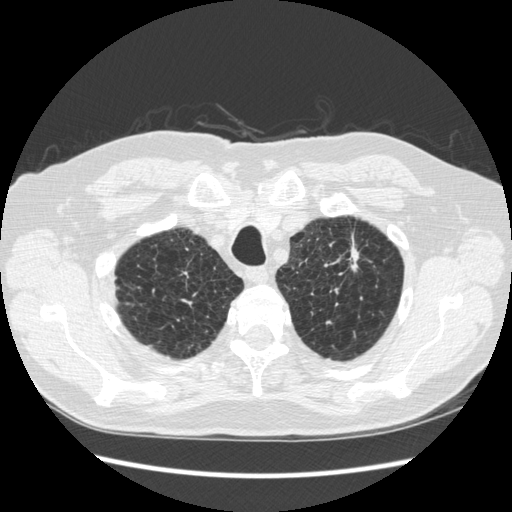
Axial slice from a low-dose chest CT screening exam; third screening round (two years after baseline); lung window (W 1500 / L -600 HU); 1.25 mm slice thickness; standard (soft-tissue) reconstruction kernel (STANDARD); 120 kVp; 512 × 512 image matrix, field of view 360 × 360 mm. Male, age 70 years at enrolment.
Lesion marked by an expert reader, bounding box <324,226,377,291> (left, top, right, bottom; pixels). The screening reader recorded 2 non-calcified nodules or masses ≥4 mm on this exam; which of them this box marks is not recorded. Later outcome: lung cancer diagnosed 92 days after this screen — squamous cell carcinoma, NOS, left upper lobe, moderately differentiated (G2), stage IA (AJCC 6th edition), 18 mm at pathology.